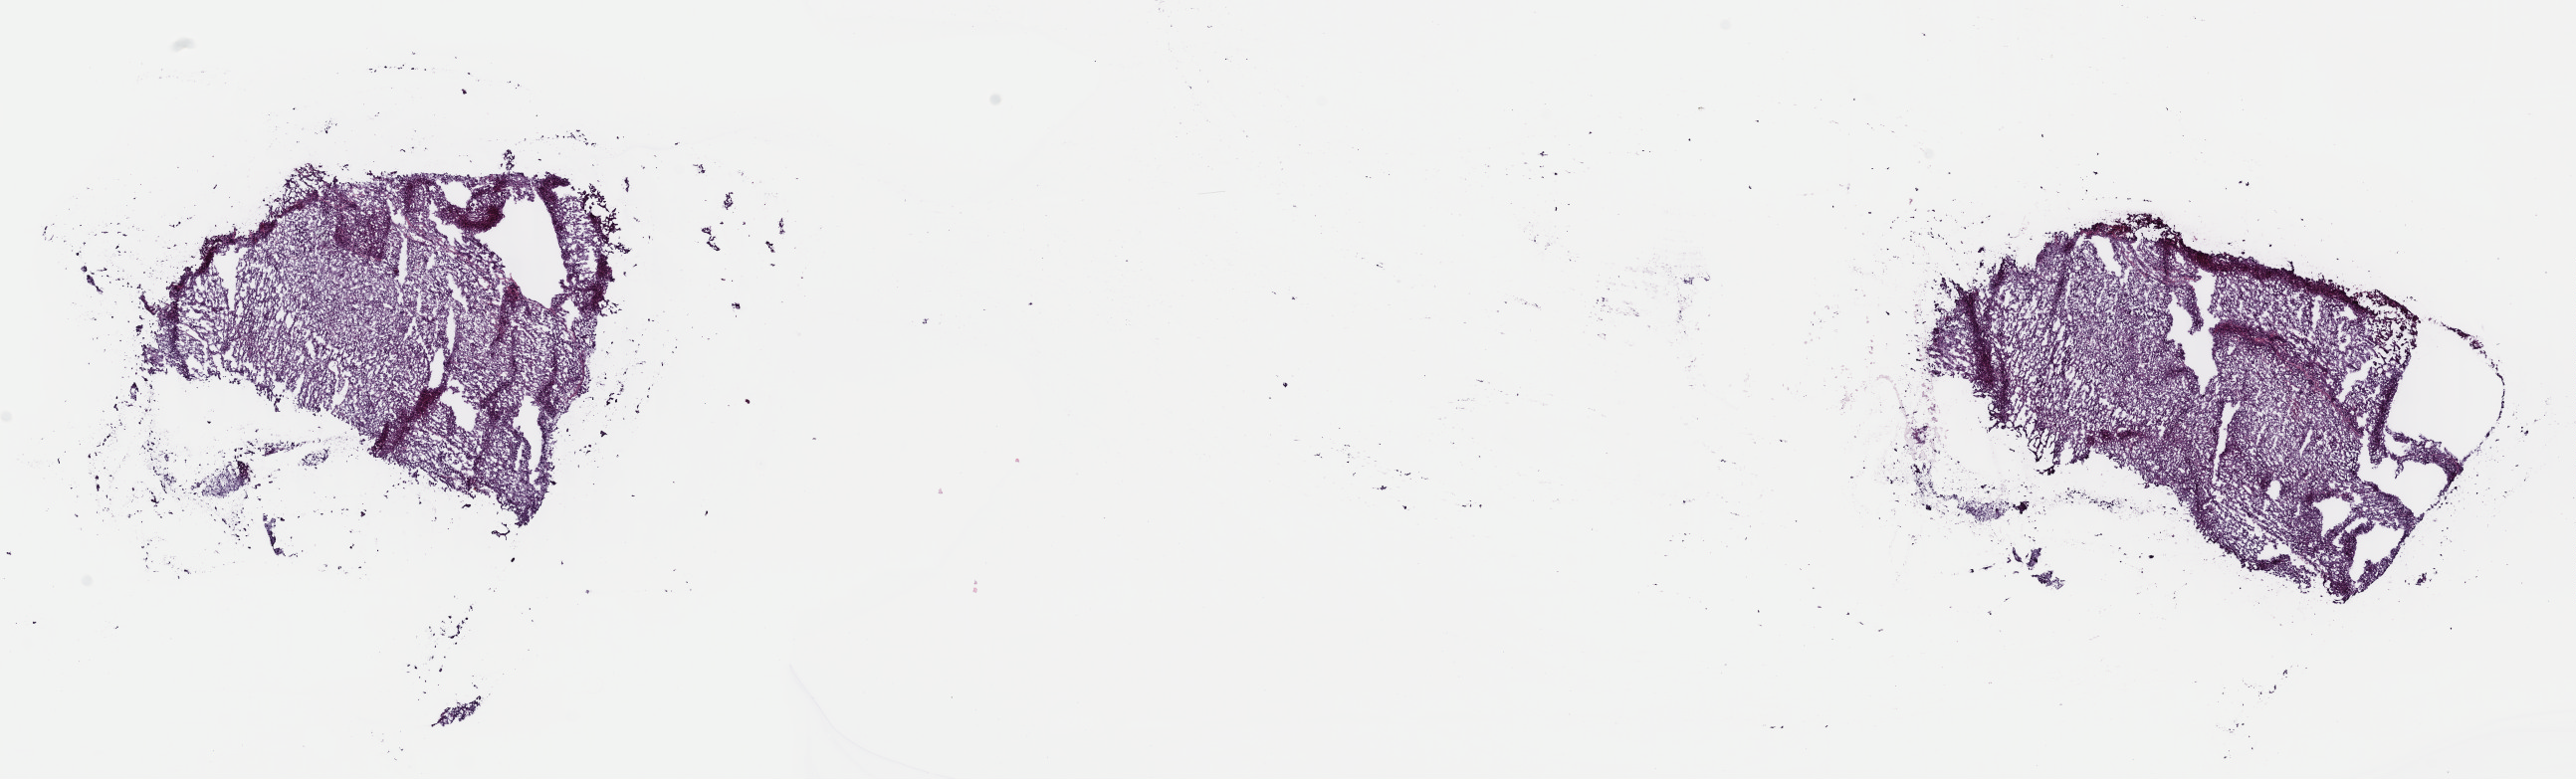
Whole-slide histology image, H&E-stained — a low-resolution overview of the entire scanned area, about 20.4 x 6.2 mm. Frozen section from the top of the tissue portion. Primary tumour sample from the adrenal cortex. Male, age 60 years at initial diagnosis. Pathologist review of this section (percent, as recorded): tumour cells 90%, tumour nuclei 95%, normal cells 0%, stromal cells 5%, necrosis 5%. Inflammatory infiltration, as recorded: lymphocyte infiltration 0%, monocyte infiltration 0%, neutrophil infiltration 0%.
Pathologic diagnosis: Adrenal cortical carcinoma (cortex of adrenal gland).